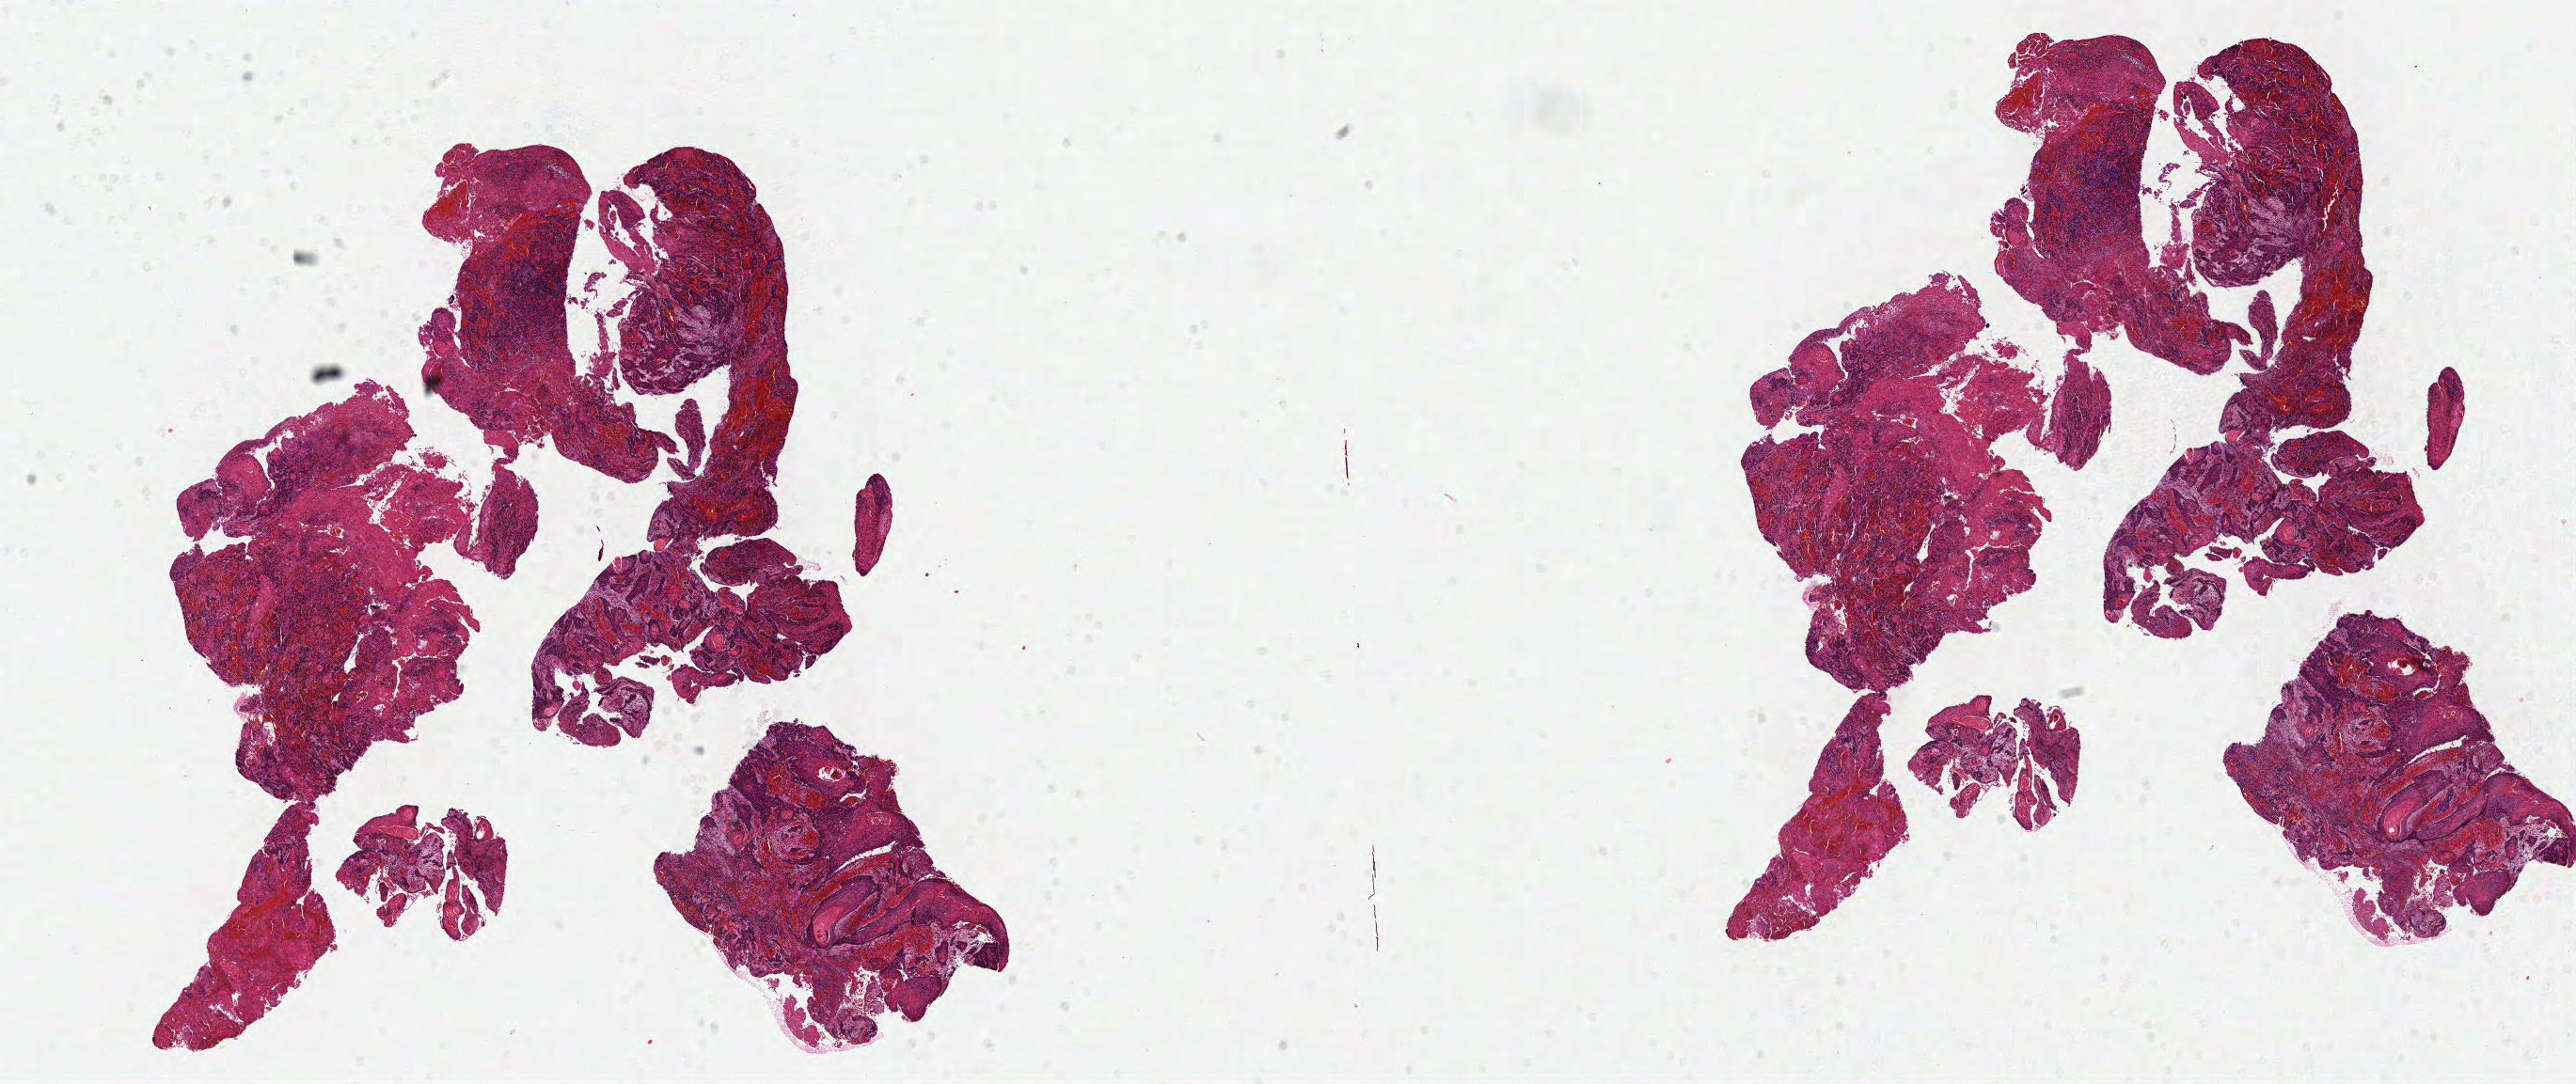
H&E-stained whole-slide image — whole scanned area (about 21.5 x 9.1 mm, acquisition: 40x scan) shown as a low-resolution overview, formalin-fixed paraffin-embedded (FFPE) diagnostic section, sample: primary tumour, head and neck. Patient: male, age at initial diagnosis 47 years.
Pathologic diagnosis: Squamous cell carcinoma, NOS.